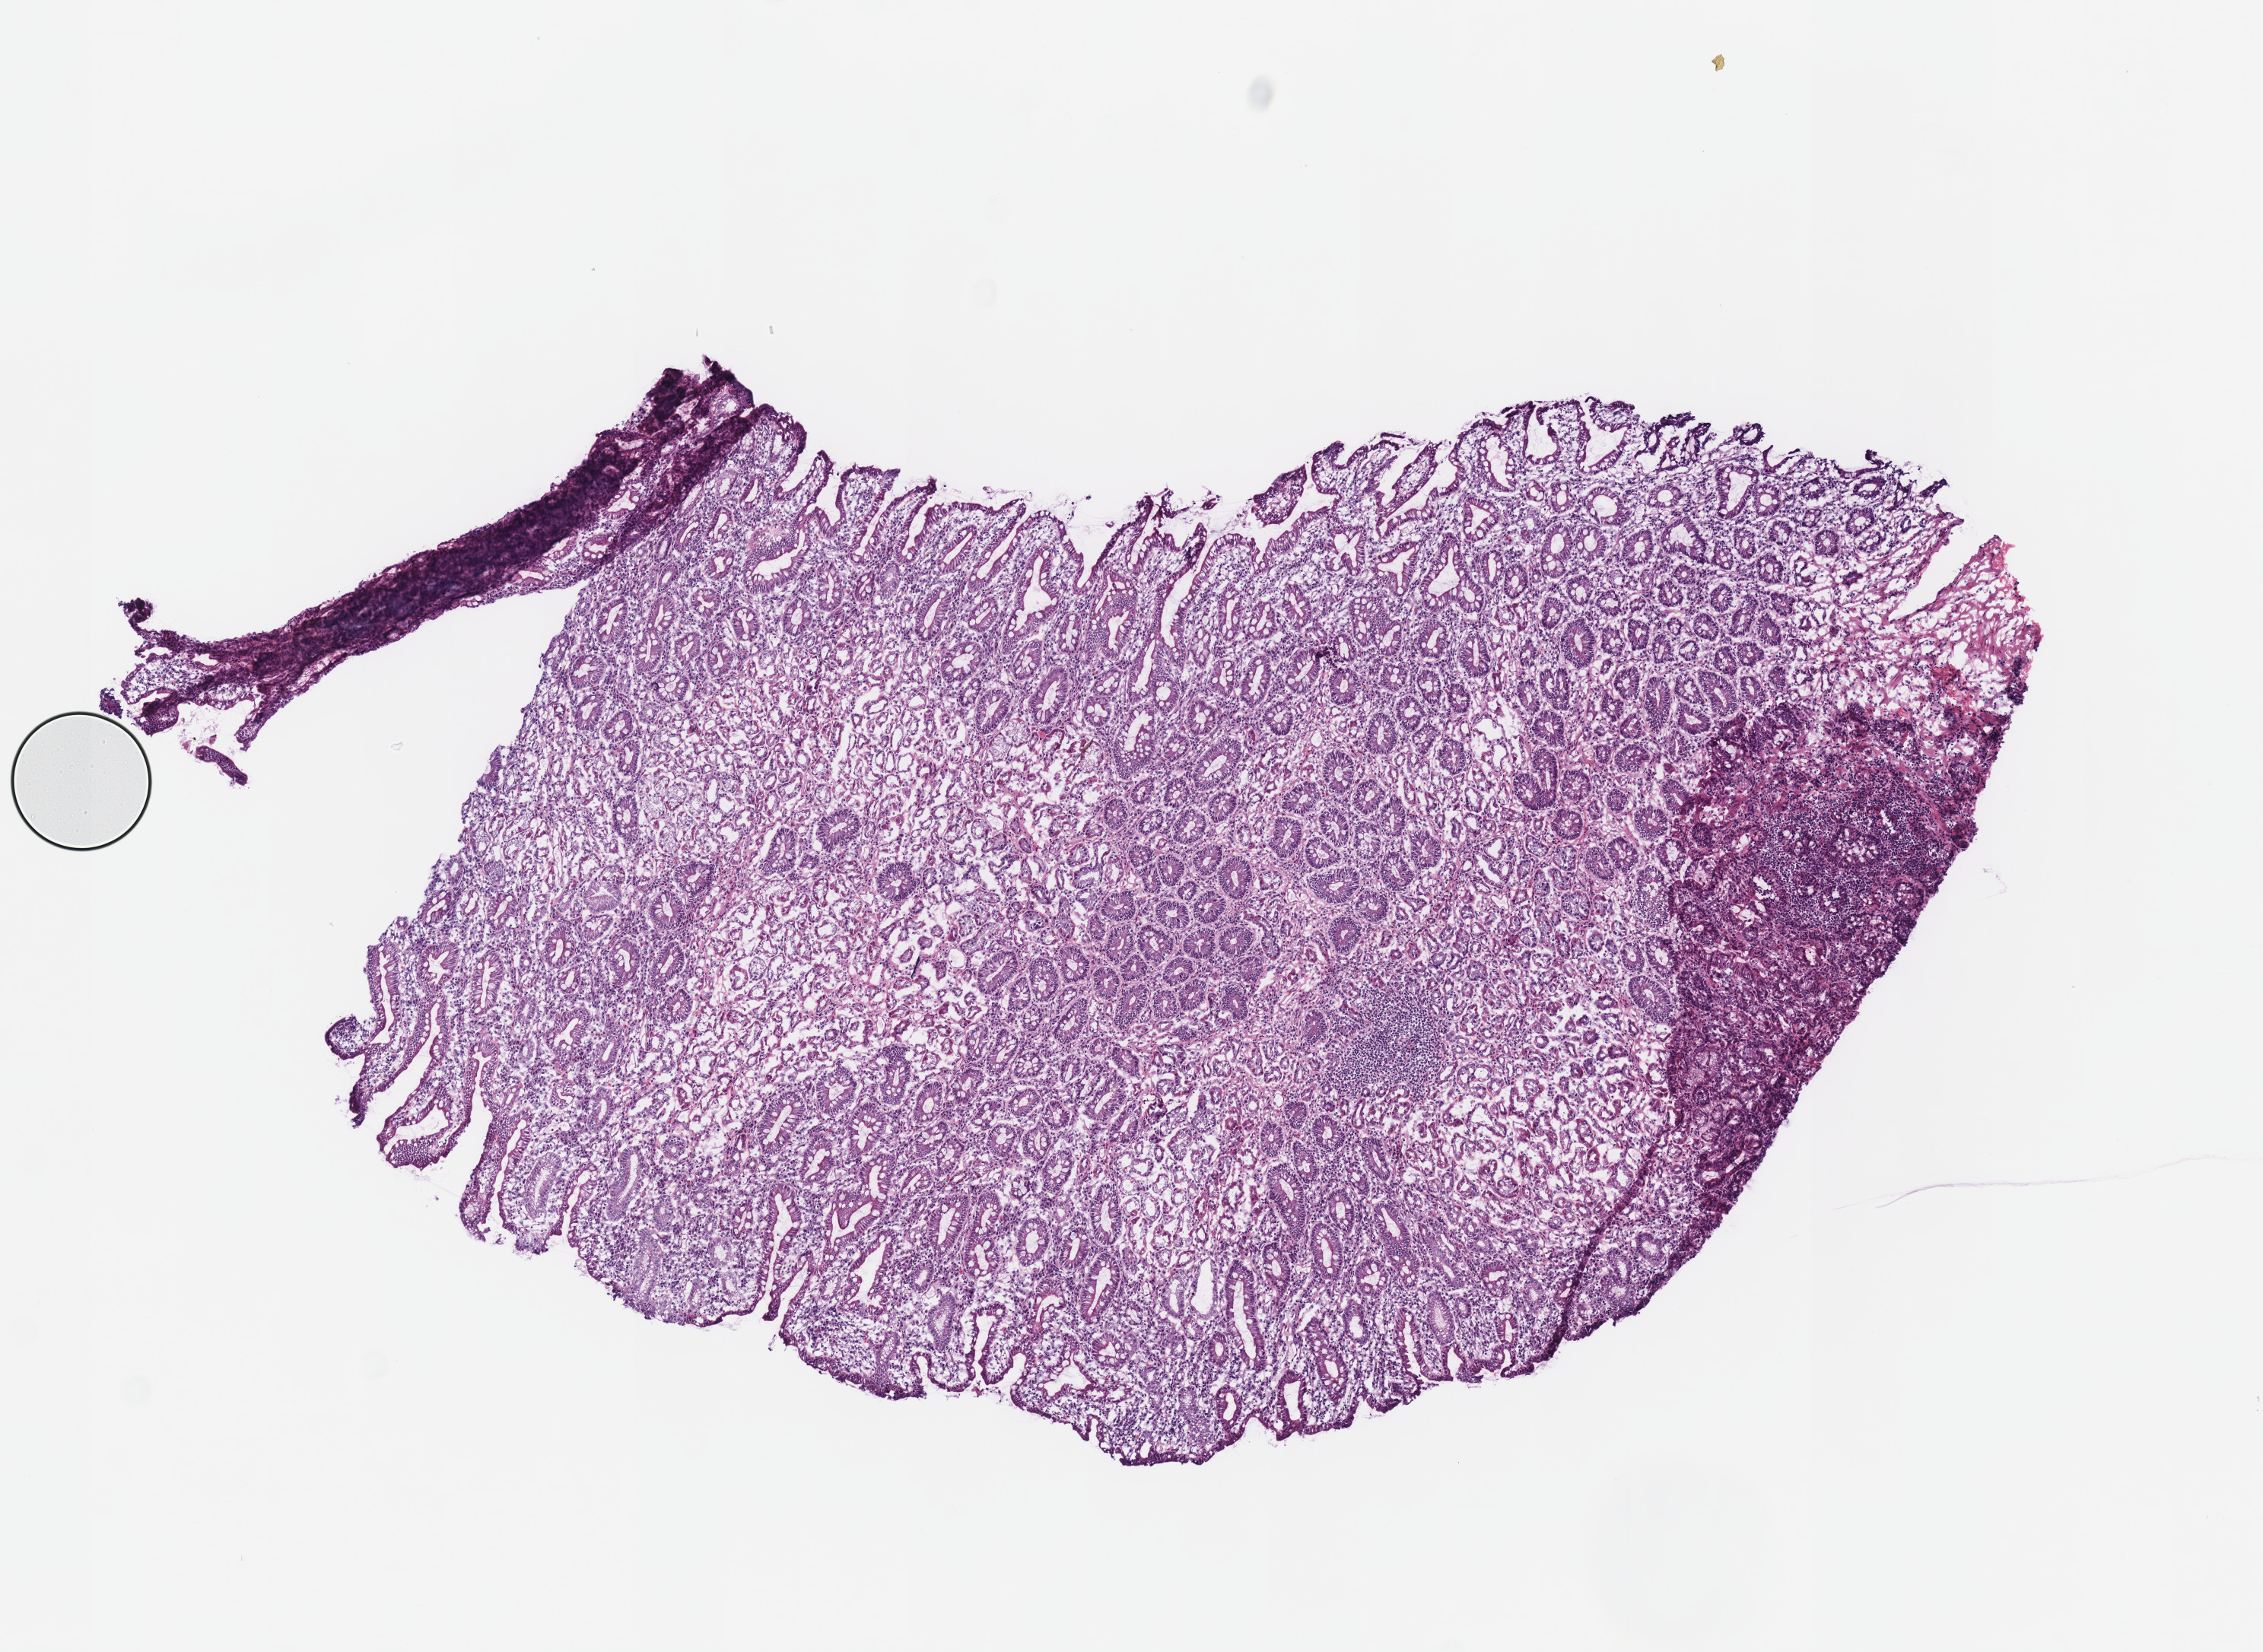
Digitized Hematoxylin and eosin (H&E) stained tissue section (whole slide) — low-resolution overview of the scanned area, about 5.9 x 4.3 mm (from a 40x scan), frozen section from the top of the tissue portion, sample: solid tissue normal (non-tumour tissue), stomach. Female patient; age at initial diagnosis 77 years.
This section: solid tissue normal sample (biorepository sample class). Patient diagnosis: Tubular adenocarcinoma (body of stomach).